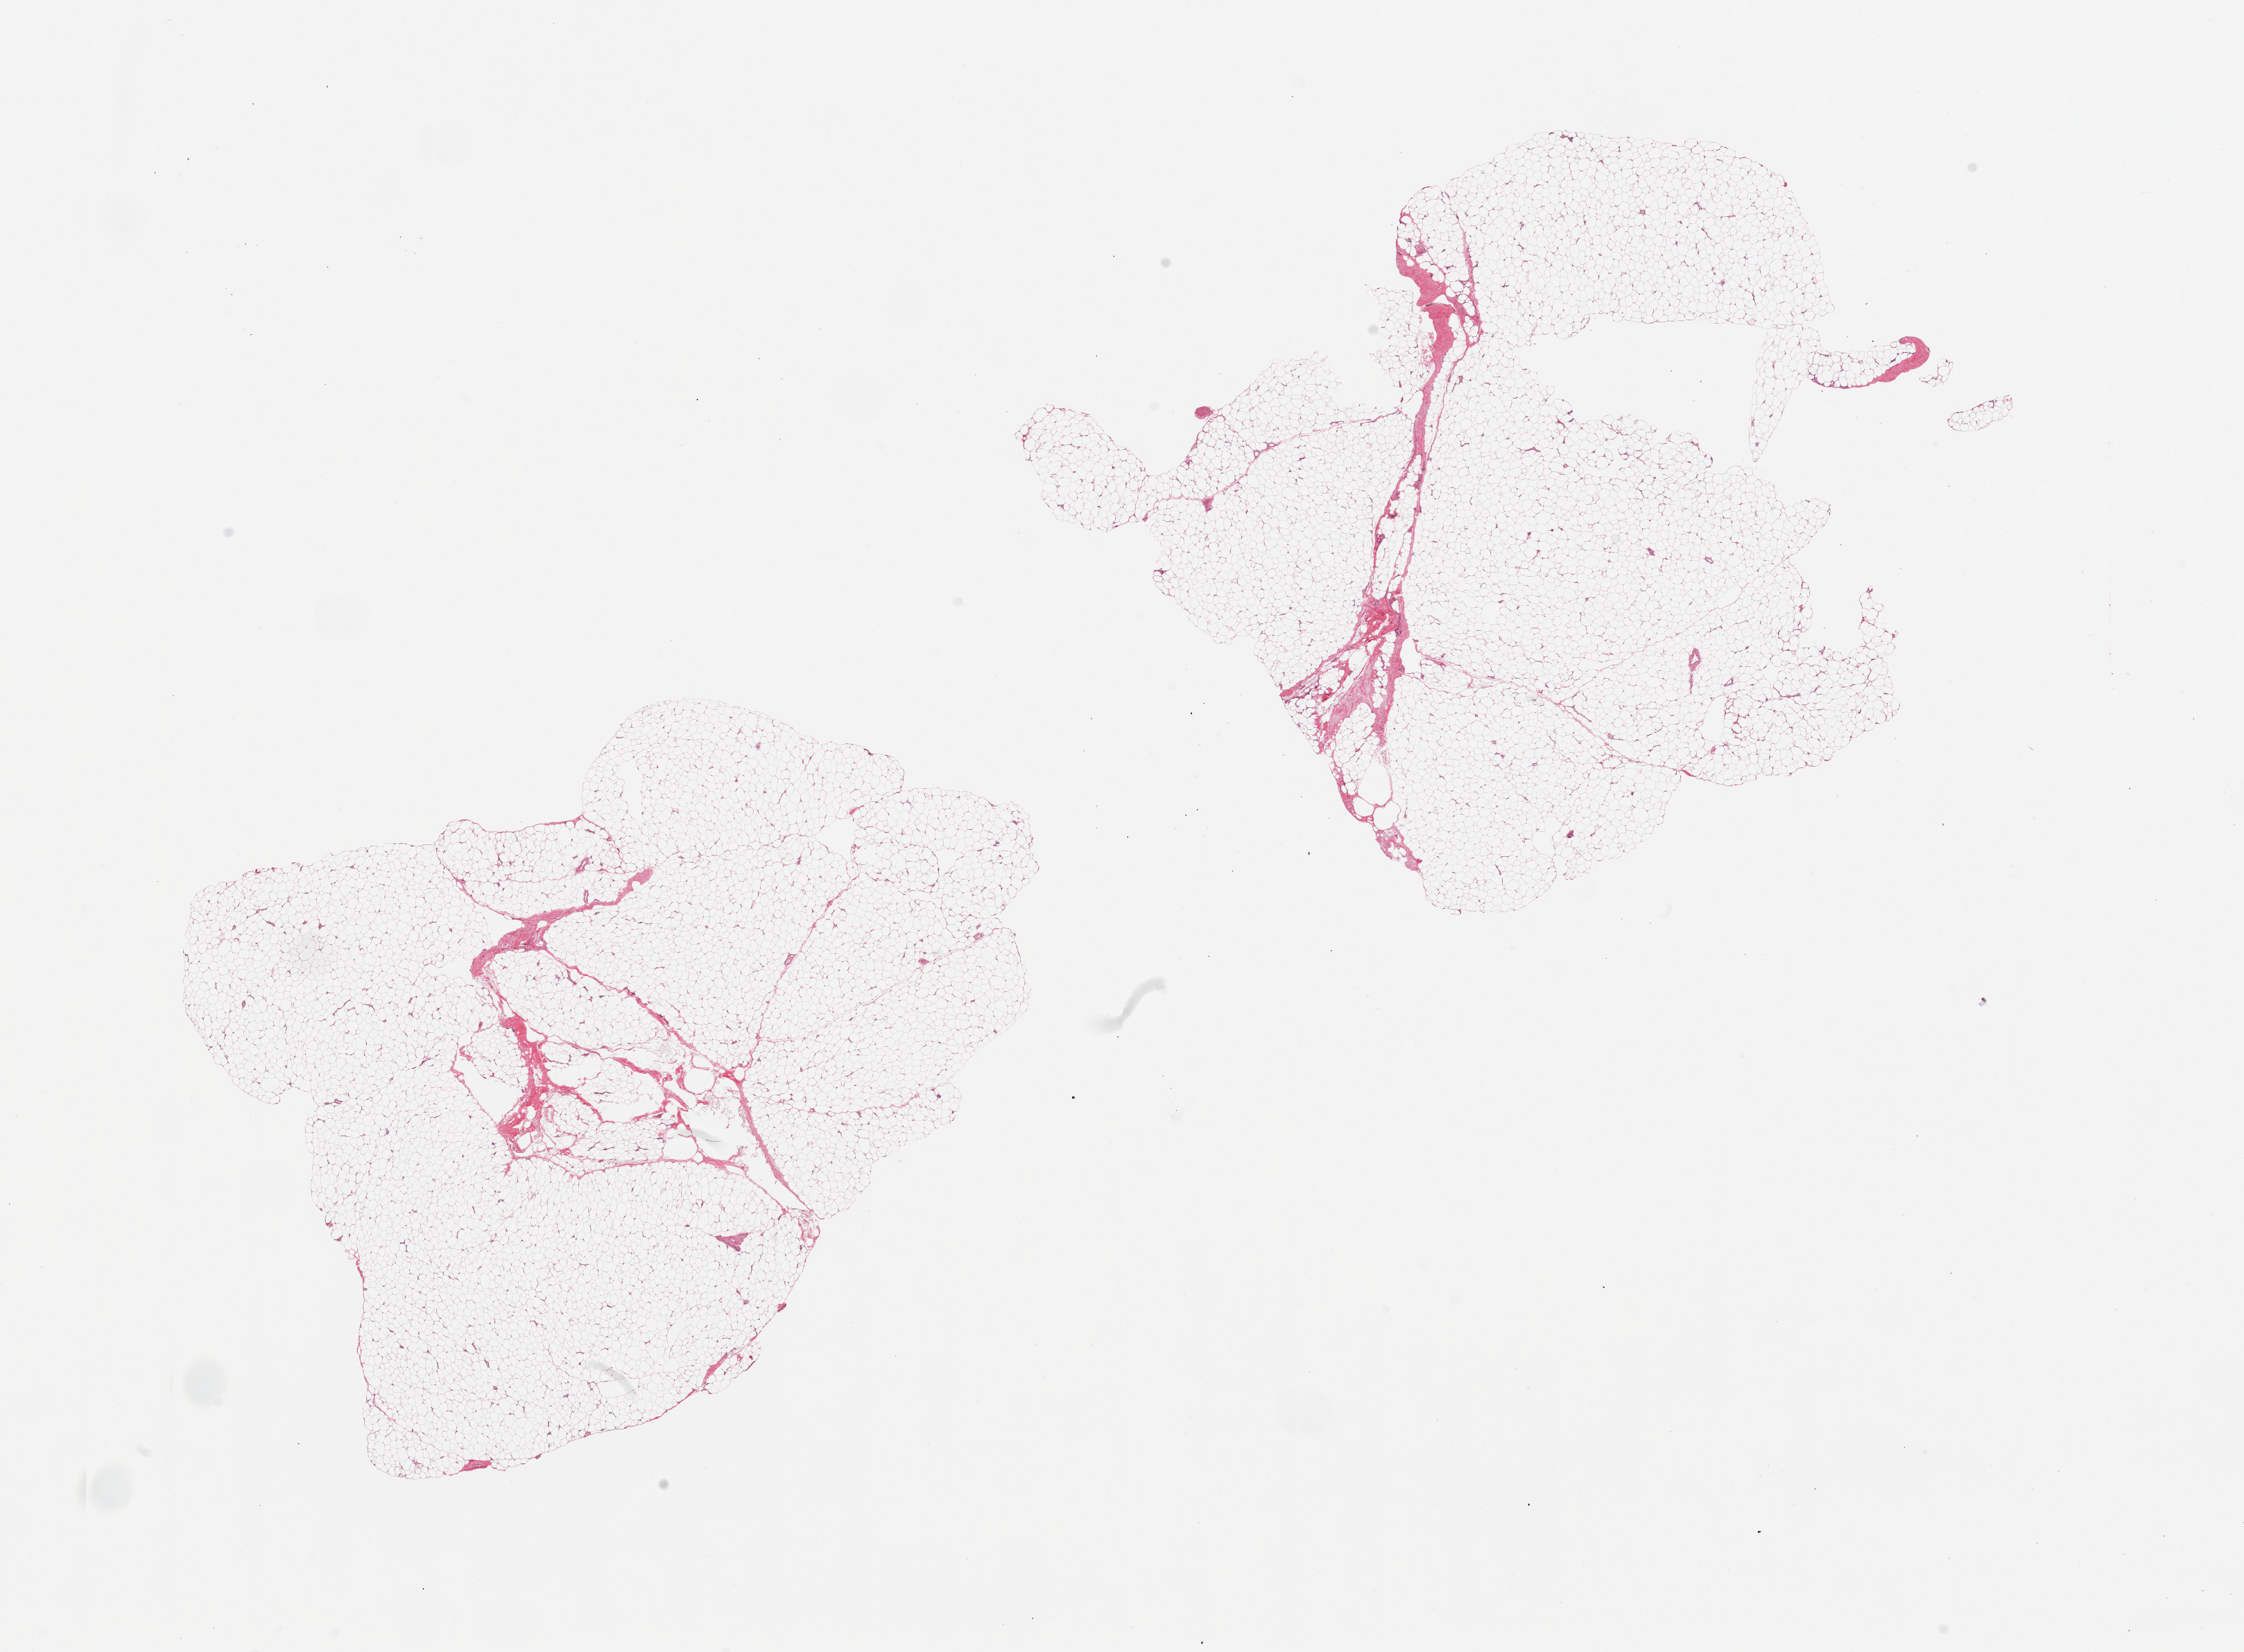
Digitized H&E-stained section, brightfield, whole scanned area (about 25.6 x 18.8 mm, acquisition: 20x scan) shown as a low-resolution overview. PAXgene-fixed paraffin-embedded (PFPE) section. Section of adipose tissue (target tissue). Donor tissue sample. Donor: female.
• pathologist's review note for this sample: 2 pieces; 2% fibrous content